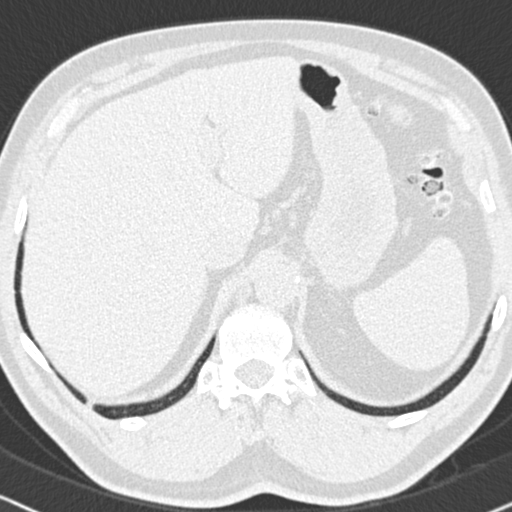
Chest CT (low-dose screening protocol), one axial image, first (baseline) screen, lung window (W 1500 / L -600 HU), 2 mm slice thickness, 512 × 512 image matrix, field of view 325 × 325 mm. Male, age 63 years at enrolment. Former smoker at enrolment.
Expert reader's lesion annotation, bounding box <71,392,104,419> (left, top, right, bottom; pixels). Screening reader's record for this exam: no non-calcified nodule ≥4 mm recorded. Official screen result: negative screen, no significant abnormalities. Later outcome: lung cancer diagnosed 626 days after this screen (after the second annual screen) — adenocarcinoma, NOS, right lower lobe, moderately differentiated (G2), stage IIIB (AJCC 6th edition), 17 mm at pathology.